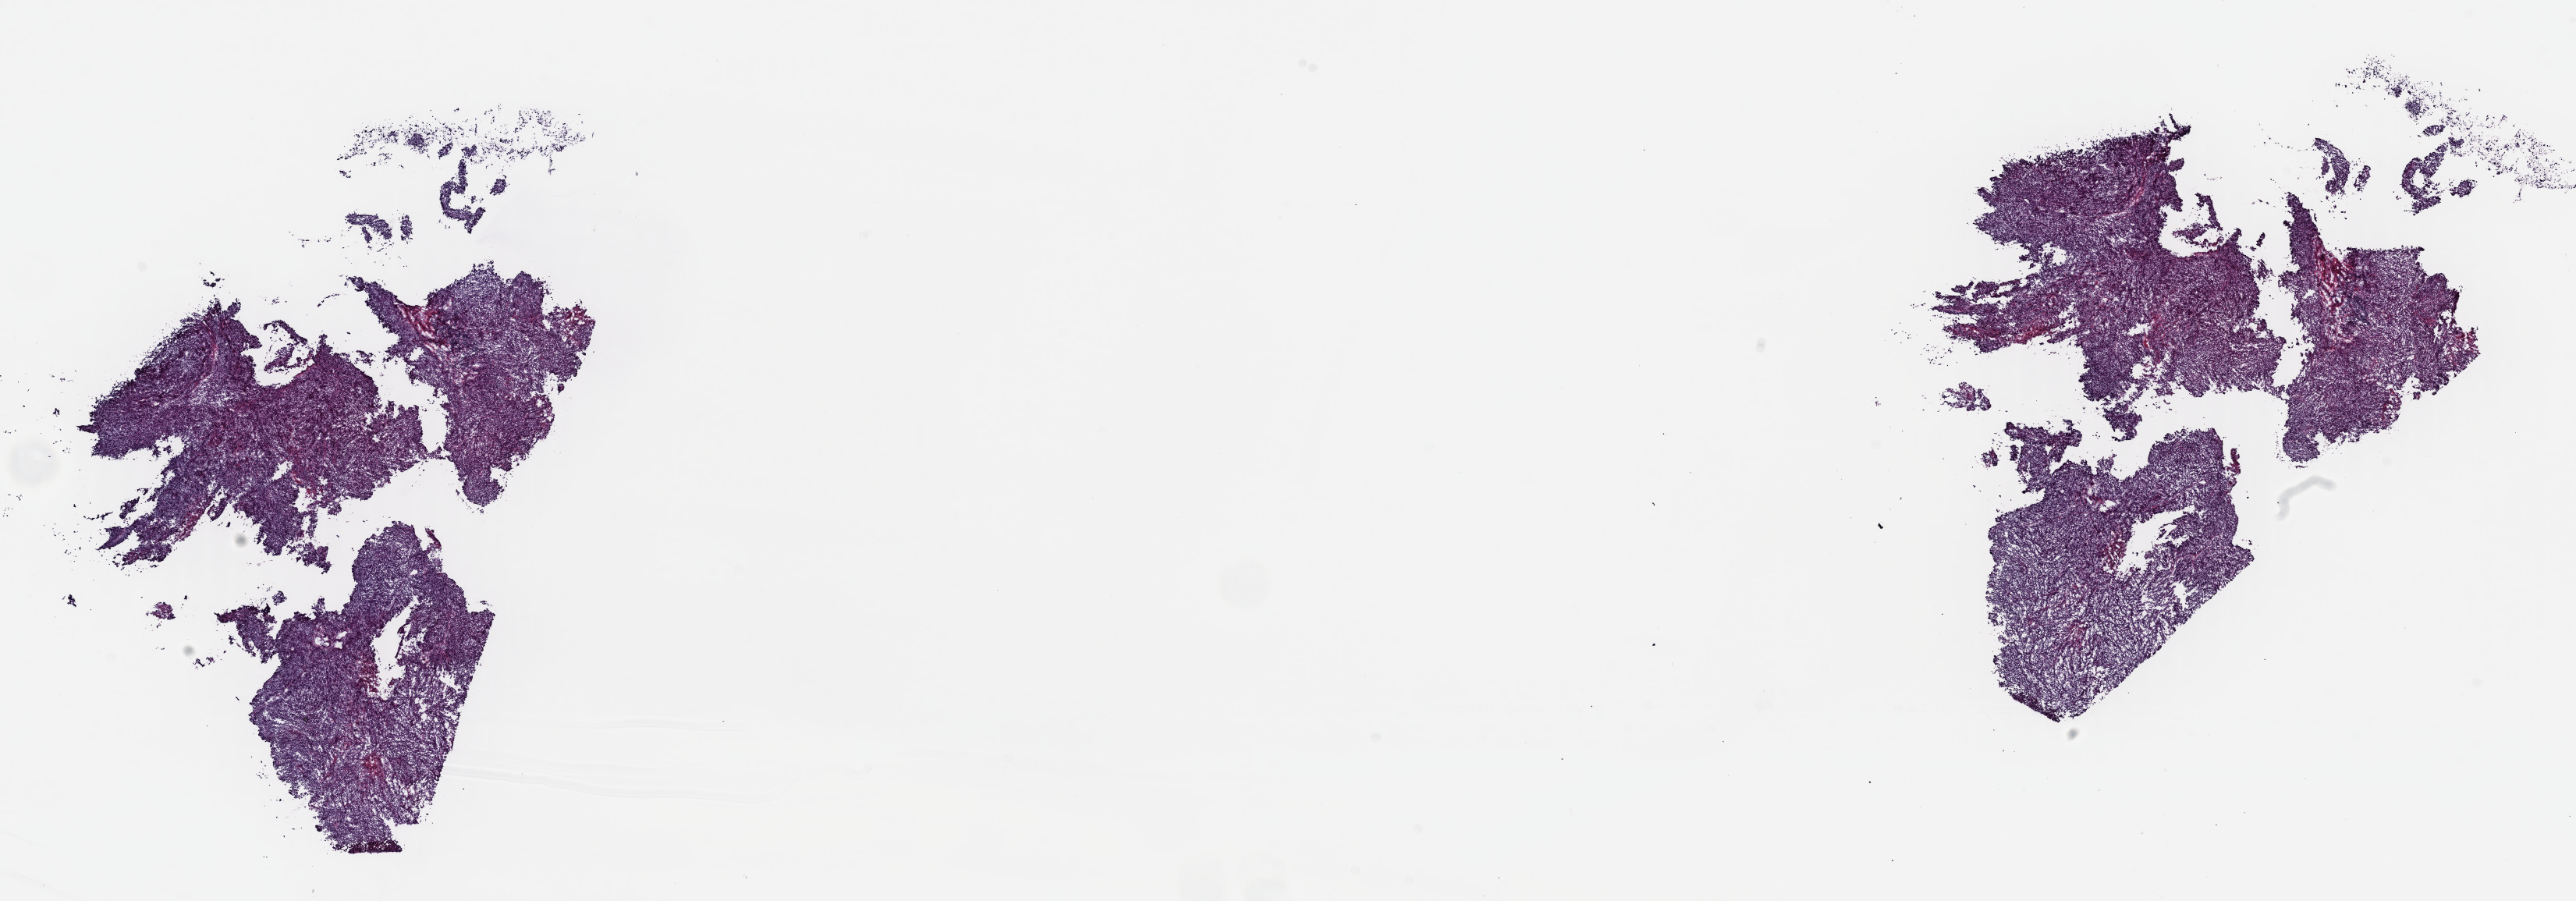
Whole-slide histology image, H&E-stained — shown as a low-resolution overview of the whole scanned area (about 26.0 x 9.1 mm, from a 40x scan). Frozen section from the top of the tissue portion. Metastatic tumour sample, sampled site: lymph node. Female patient; age at initial diagnosis 54 years. Composition of this section per pathologist review: tumour cells 90%, tumour nuclei 90%, normal cells 0%, stromal cells 9%, necrosis 1%. Inflammatory infiltration, as recorded: lymphocyte infiltration 1%, monocyte infiltration 1%, neutrophil infiltration 0%.
This section: metastatic tumour tissue. Patient diagnosis: Malignant melanoma, NOS.